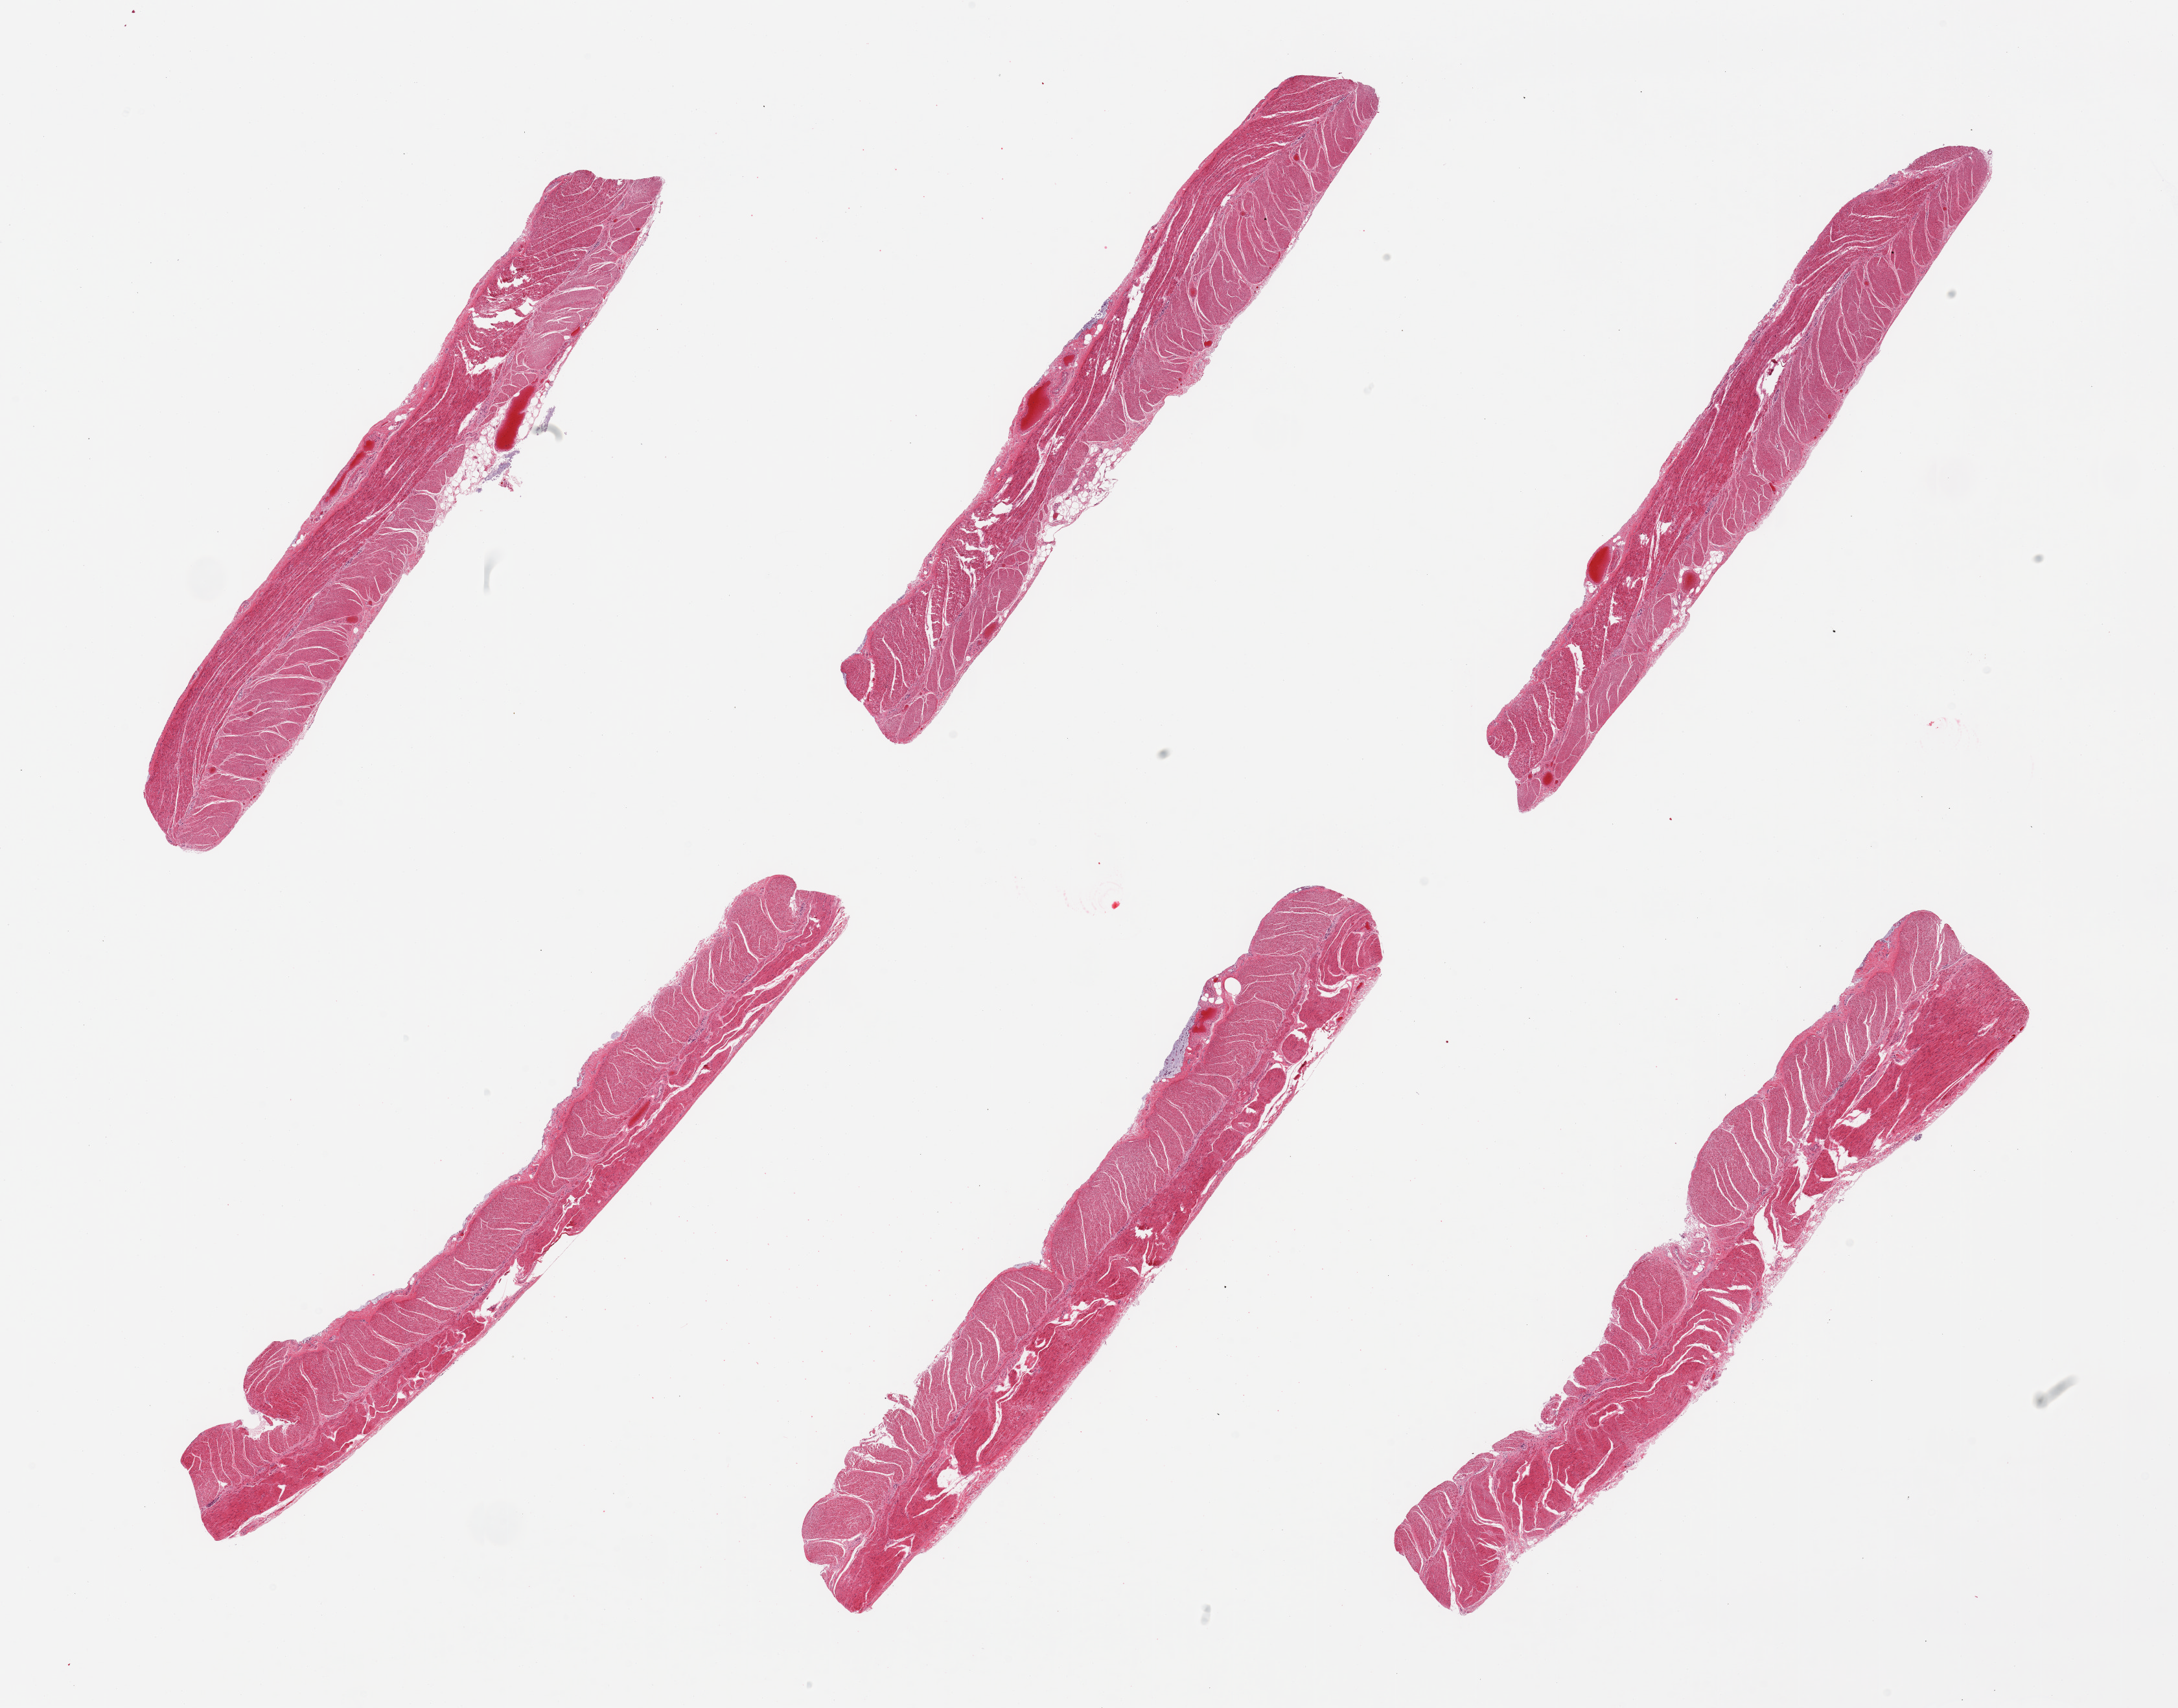
Hematoxylin and eosin (H&E) whole-slide image, brightfield, whole scanned area (about 26.6 x 20.8 mm, from a 20x scan) shown as a low-resolution overview. PAXgene-fixed, paraffin-embedded tissue. Section of sigmoid colon (target tissue). Donor tissue sample. Male donor.
Review note (as recorded): 6 pieces; well dissected muscle.